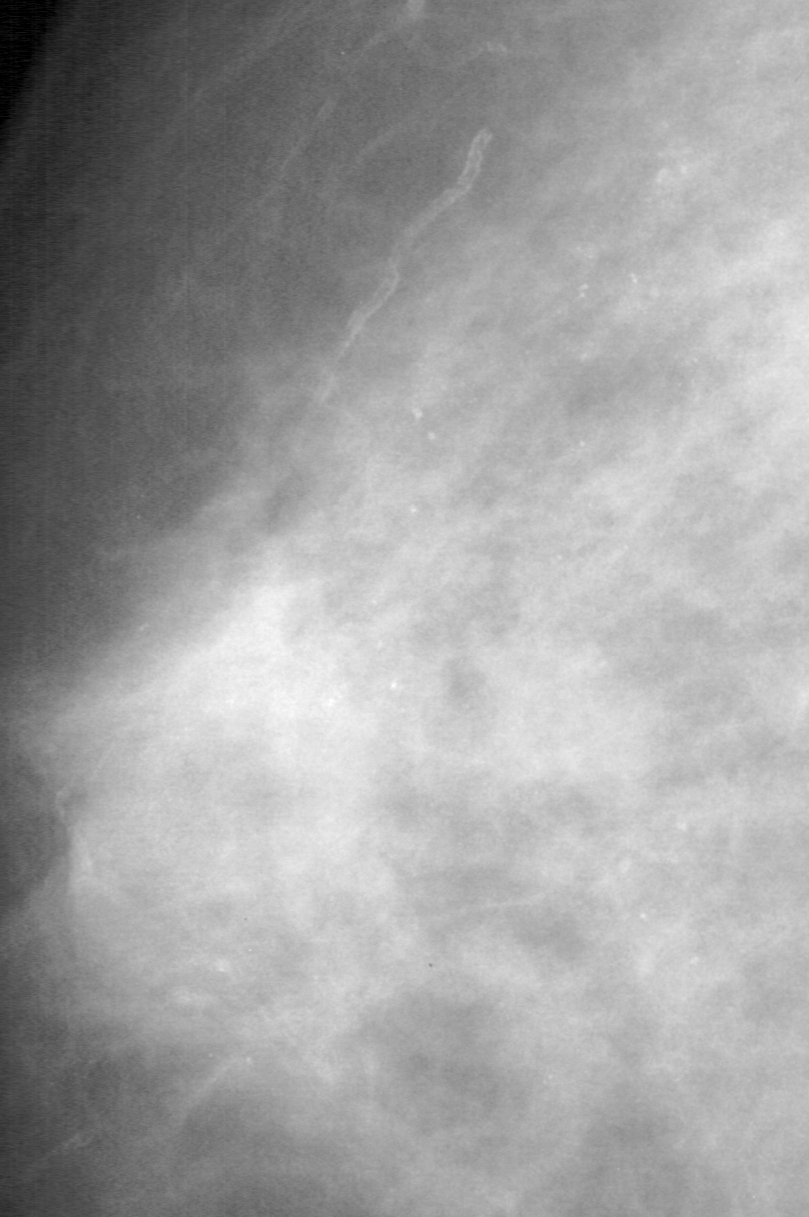
Cropped region of a digitized screen-film mammogram centred on a radiologist-marked abnormality; left breast; CC view; BI-RADS breast density category 4 (scale 1–4).
- Marked abnormality: calcifications, morphology punctate / amorphous, distribution regional; BI-RADS assessment category 4; subtlety rating 3 on a 1 (subtle) to 5 (obvious) scale; pathology result (as recorded, not read from the image): benign.